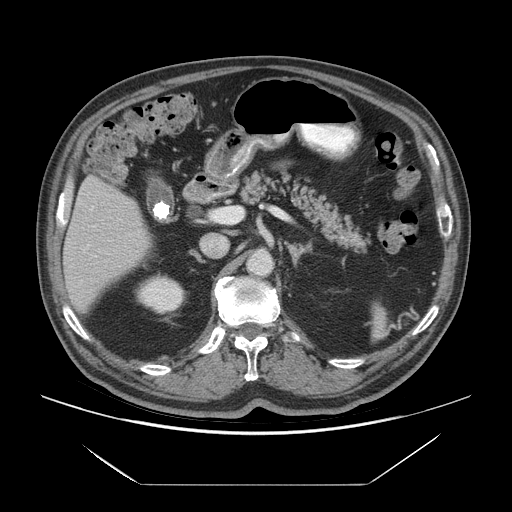
Contrast-enhanced abdominal CT (liver protocol), one axial slice; slice 32 of 75 in the series (ordered by position); reconstruction kernel STANDARD; 140 kVp; soft-tissue window (W 400 / L 40 HU); 512 × 512 image matrix, field of view 420 × 420 mm. From the clinical record (not read from this slice): diagnosis: hepatocellular carcinoma (patient treated with transarterial chemoembolisation; whether this scan precedes or follows treatment is not stated here); TNM stage (as recorded): Stage-I; Child-Pugh class: A; tumour differentiation: well differentiated.
Outlined on this slice (semi-automatic segmentation, software-assisted and operator-edited):
- liver parenchyma outside the tumour (the mass and vessels are separate outlines, so this box may not span the whole liver): bounding box (x1, y1, x2, y2) in pixels: (64, 176, 150, 312)